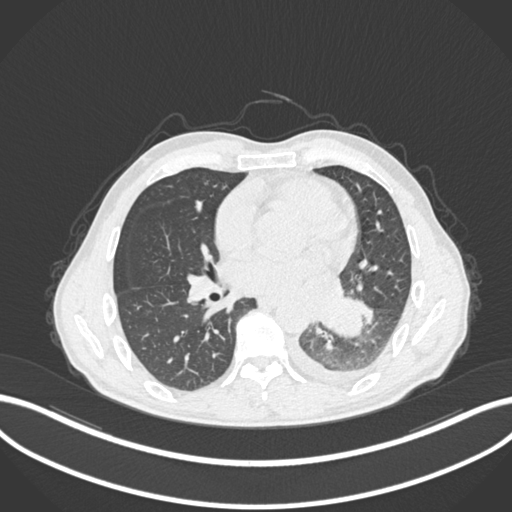
Chest CT, one axial slice; position 112 of 222 along the scan axis; reconstruction kernel B30f; 120 kVp; lung window (W 1500 / L -600 HU); 1 mm slice thickness; 512 × 512 image matrix, field of view 400 × 400 mm. Patient: male, 47 years. From the clinical record (not read from this slice): clinical TNM (as recorded): T3 N1 M1c.
Structures marked on this image (bounding box drawn by a radiologist):
- lung tumour (recorded histology: small cell carcinoma): box from (x=320, y=294) to (x=365, y=339) px